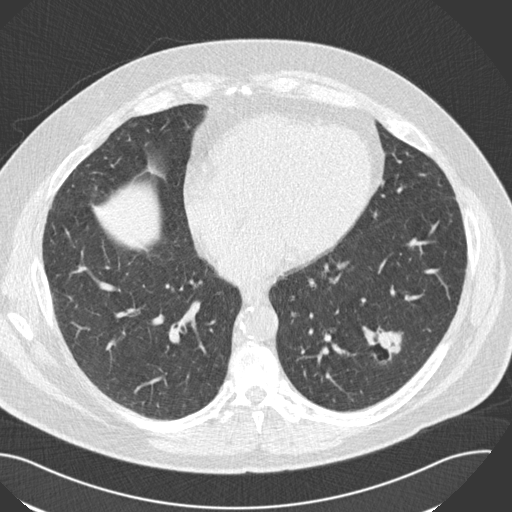
Low-dose screening chest CT, axial slice. Third annual screen. Lung window (W 1500 / L -600 HU). 2 mm slice thickness. Standard (soft-tissue) reconstruction kernel (B30f). Slice 83 of 153 in the series. 512 × 512 image matrix, field of view 394 × 394 mm. Male, age 57 years at enrolment. Current smoker at enrolment.
• Expert-annotated lung lesion, box from (x=349, y=316) to (x=418, y=373) px.
• The exam's reader record, not a measurement of the box and not confirmed to be the same lesion: non-calcified nodule or mass ≥4 mm, left lower lobe, 22 × 18 mm, poorly defined margins, soft tissue attenuation, pre-existing on the prior screen: yes; interval growth: yes.
• Official screen result: positive, other.
• Lung cancer was diagnosed 124 days after this screen: squamous cell carcinoma, NOS, left lower lobe, moderately differentiated (G2), stage IA (AJCC 6th edition), 22 mm at pathology.